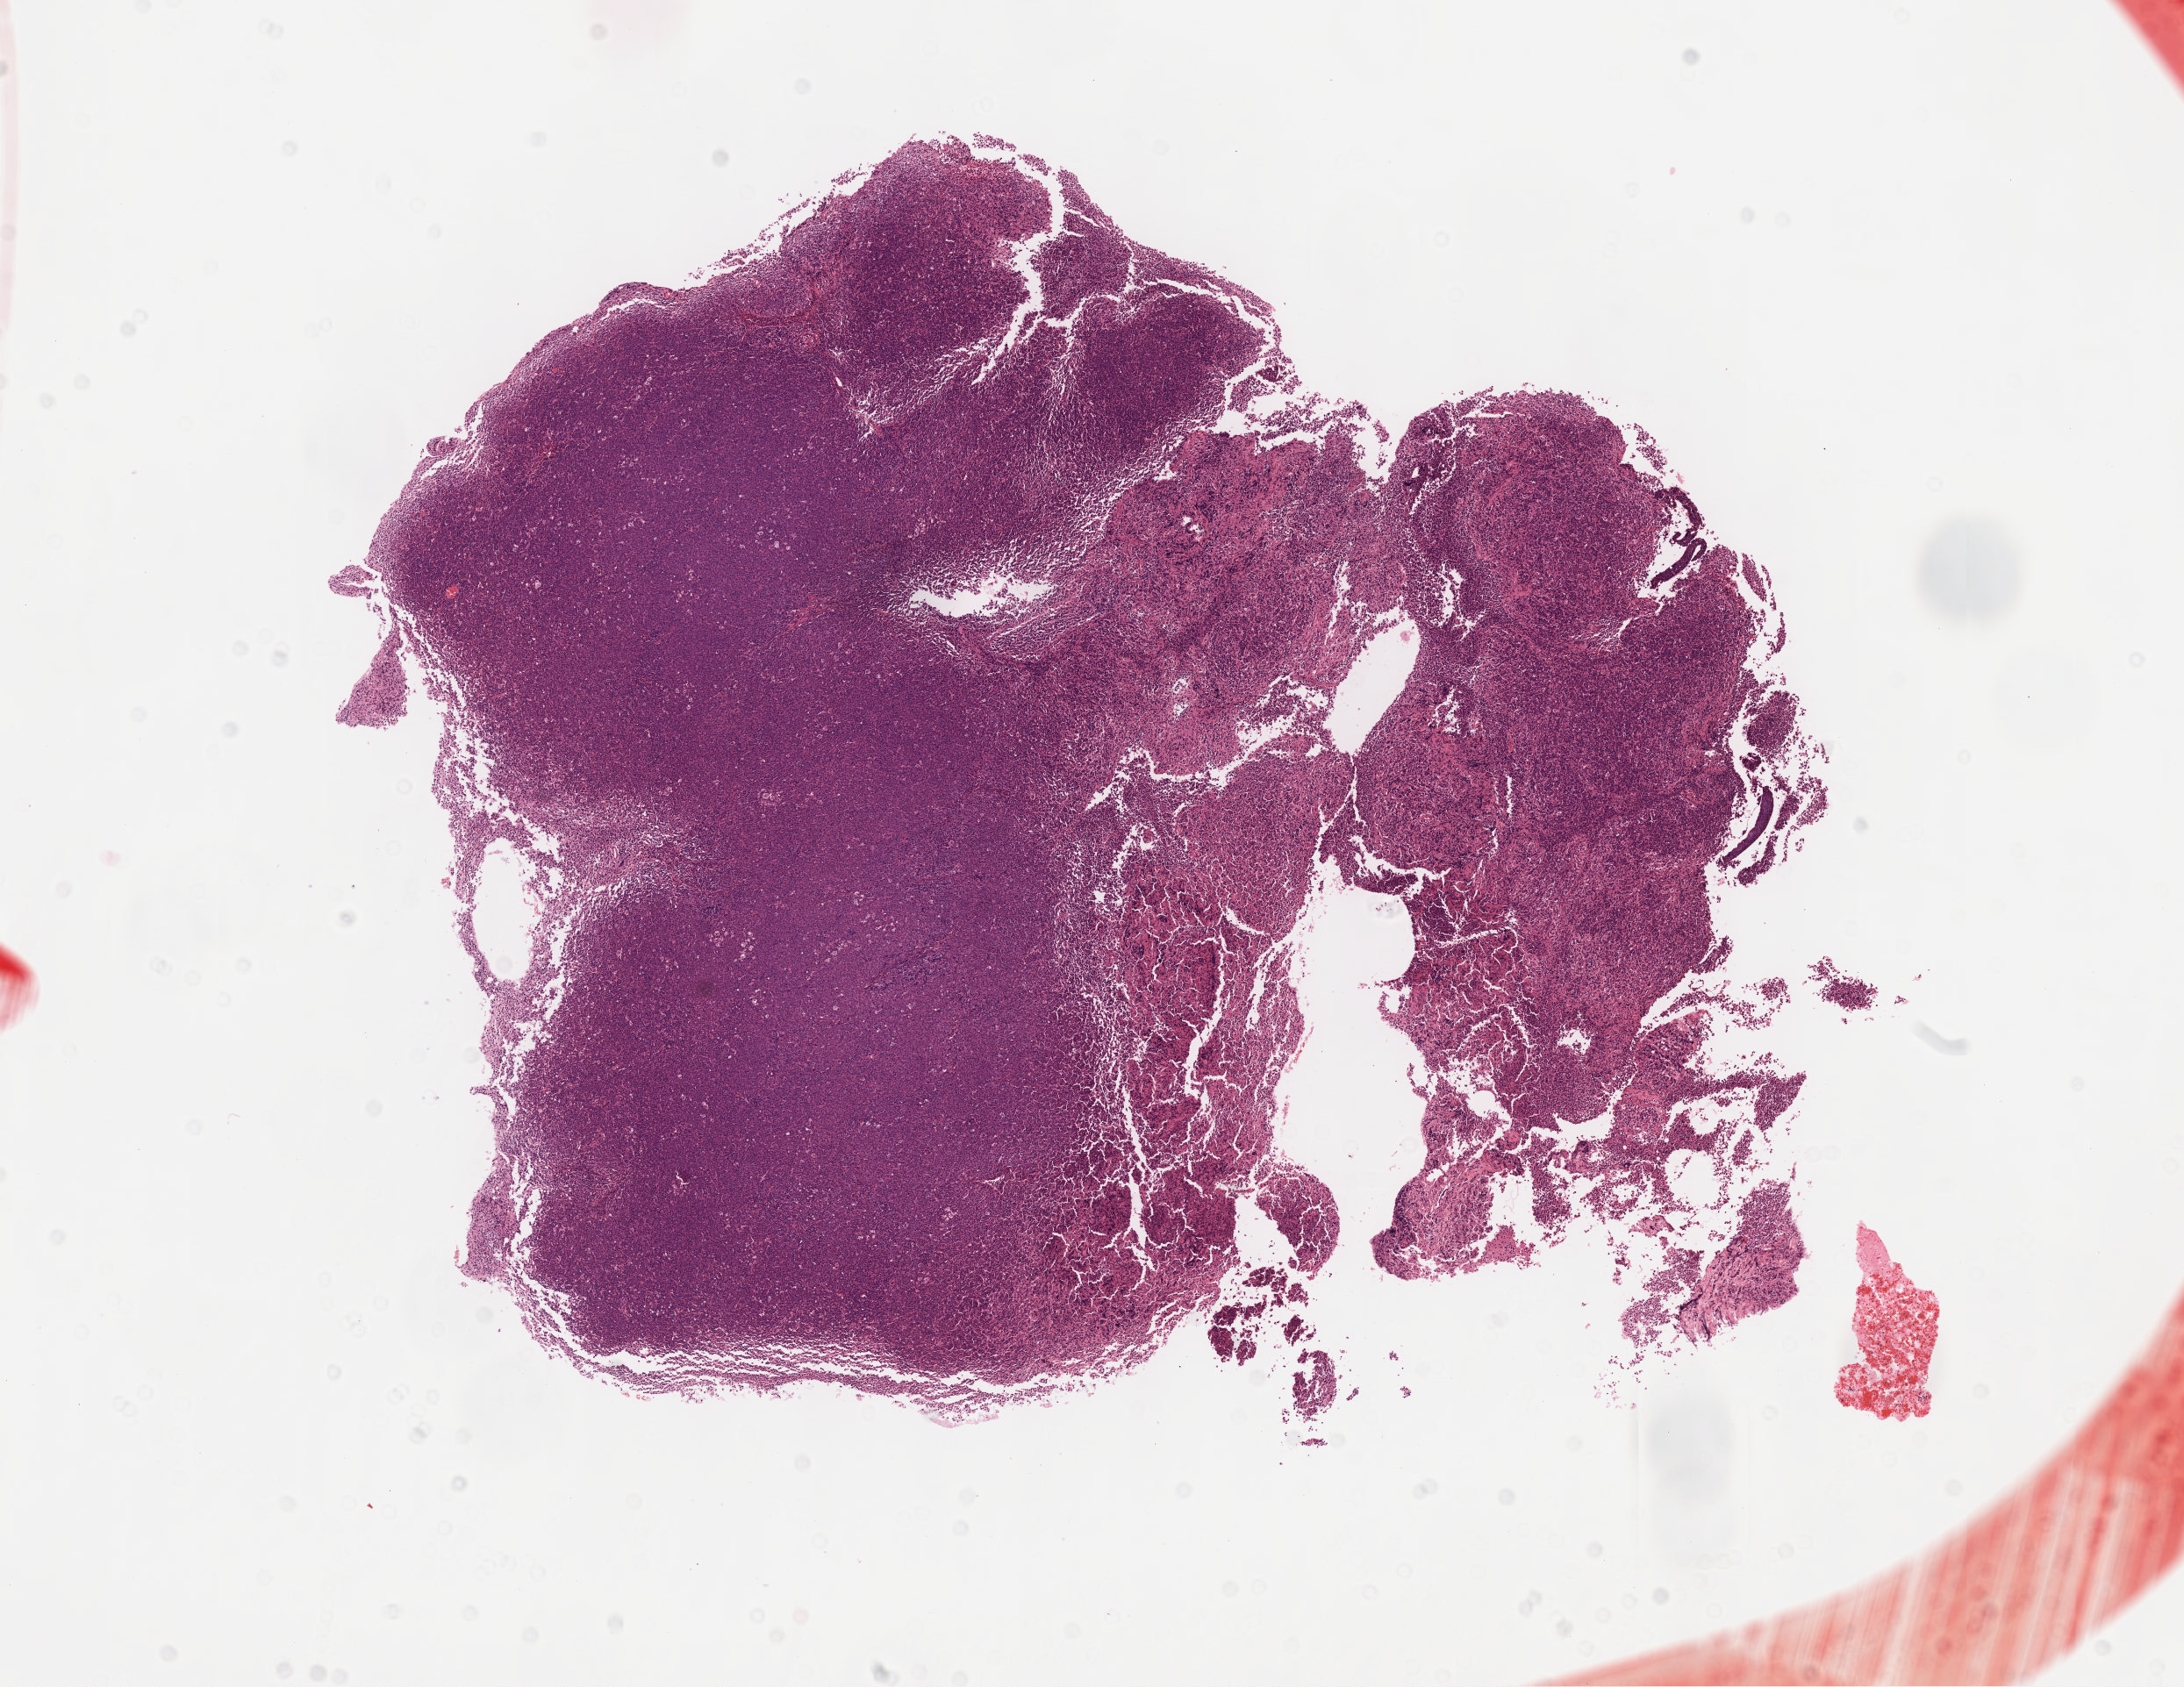
Digitized H&E tissue section (whole slide) — low-resolution overview of the scanned area, about 10.1 x 7.8 mm. FFPE section. Sample: primary tumour, lymphoid tissue. Female patient; age at initial diagnosis 61 years.
Pathologic diagnosis: Diffuse large B-cell lymphoma, NOS.